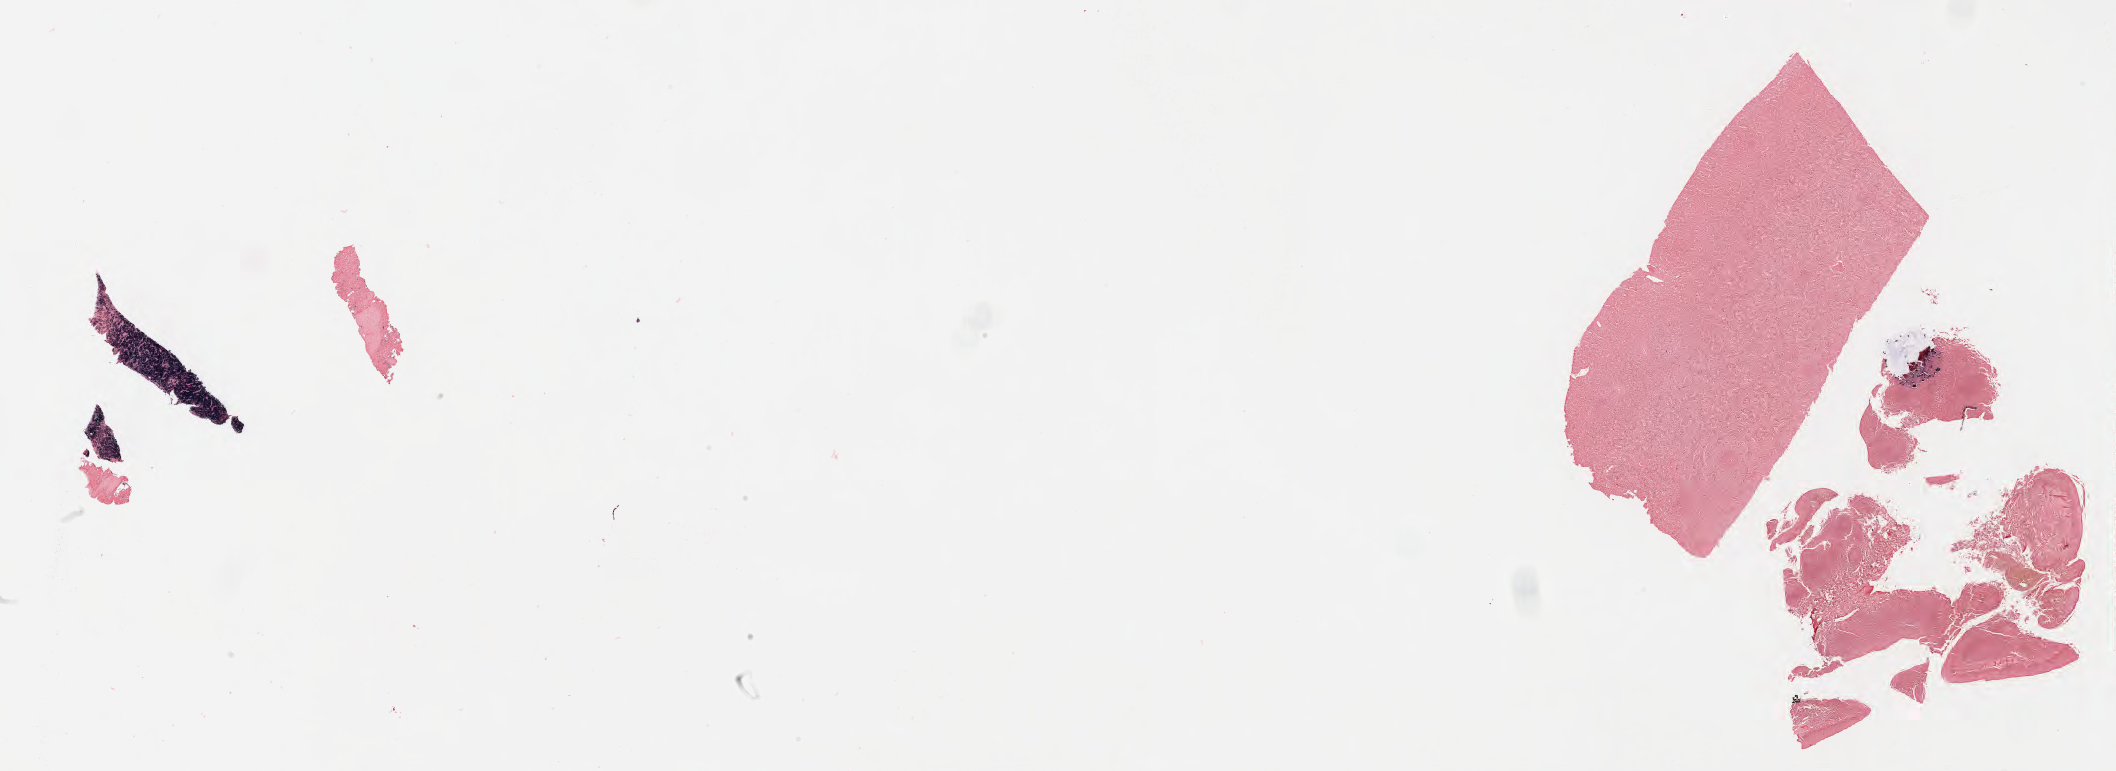
Whole-slide image, Epstein–Barr virus-encoded RNA (EBER) in-situ hybridisation — shown as a low-resolution overview of the whole scanned area (about 34.2 x 12.5 mm); specimen: tumor tissue. Patient: male, 13 years old.
Diagnosis: Diffuse large B-cell lymphoma, NOS.